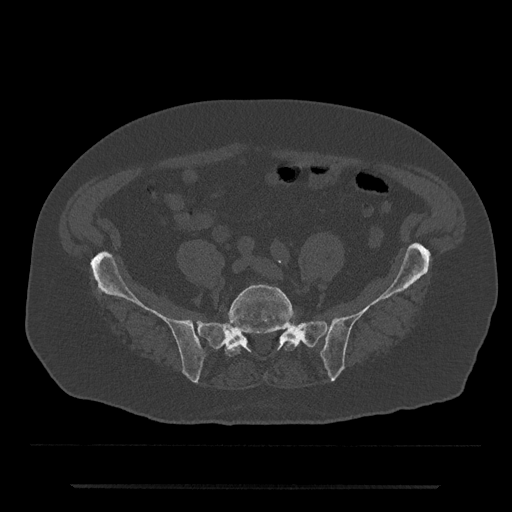
CT including the spine, one axial slice; position 261 of 797 along the scan axis; bone window (W 1800 / L 400 HU); 512 × 512 image matrix. Male patient, age 80 years. Case-level facts recorded for this patient, not image findings: primary cancer: prostate; vertebrae with lytic lesions (as recorded): L1, T11.
Outlined on this slice (semi-automatic segmentation, software-assisted and operator-edited):
- L5 vertebra: bounding box (x1, y1, x2, y2) in pixels: (225, 284, 293, 356)